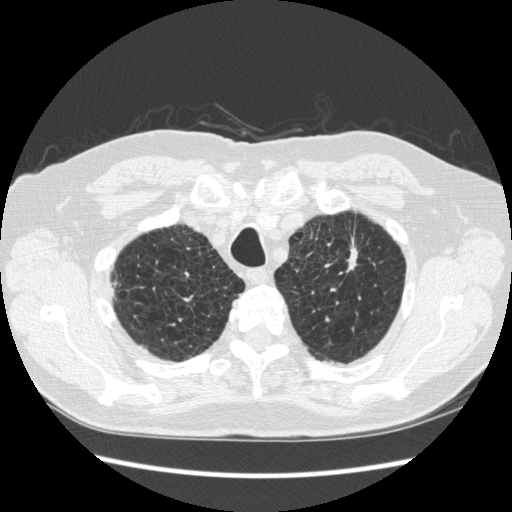
Low-dose screening chest CT, axial slice. Third screening round (two years after baseline). Lung window (W 1500 / L -600 HU). Slice 39 of 267 in the series. Male, age 70 years at enrolment.
Expert-annotated lung lesion, bounding box (x1, y1, x2, y2) in pixels: (323, 224, 376, 289). The screening reader recorded 2 non-calcified nodules or masses ≥4 mm on this exam (left upper lobe, right lower lobe); which of them this box marks is not recorded. Official screen result: positive, other.